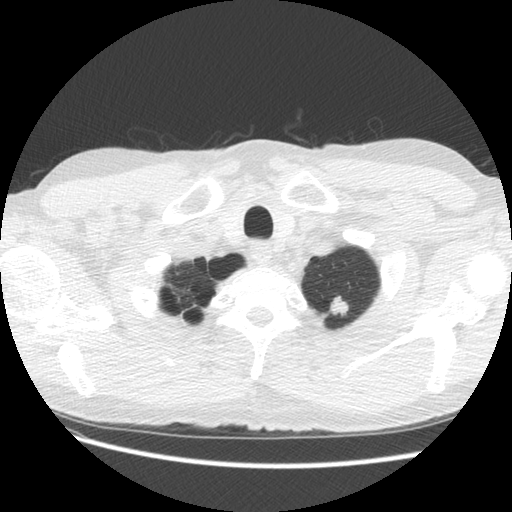
Chest CT (low-dose screening protocol), one axial image. Second screening round (one year after baseline). Lung window (W 1500 / L -600 HU). 2.5 mm slice thickness. Standard (soft-tissue) reconstruction kernel (STANDARD). Slice 118 of 131 in the series. Male participant, aged 63 years at enrolment. Former smoker at enrolment.
Expert reader's lesion annotation, box from (x=317, y=284) to (x=363, y=323) px. The screening reader recorded 2 non-calcified nodules or masses ≥4 mm on this exam (left upper lobe, right lower lobe); which of them this box marks is not recorded. Official screen result: positive, other. Lung cancer was diagnosed 104 days after this screen: adenocarcinoma, NOS, left upper lobe, moderately differentiated (G2), stage IB (AJCC 6th edition), 14 mm at pathology.